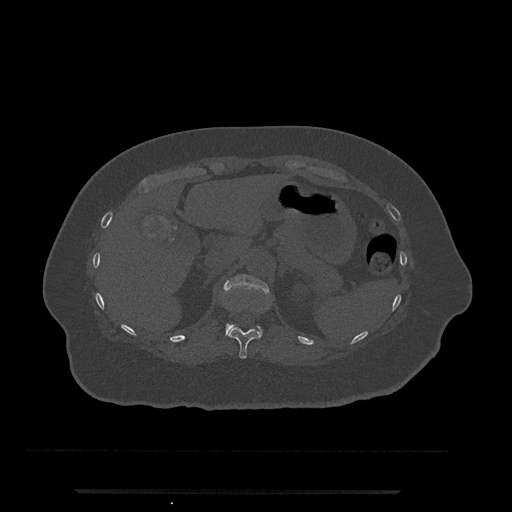
CT including the spine, one axial slice; position 205 of 797 along the scan axis; bone window (W 1800 / L 400 HU); 0.5 mm slice thickness; 512 × 512 image matrix, field of view 440 × 440 mm. Patient: female, 51 years. From the clinical record (not read from this slice): primary cancer: neuro.
Annotated regions visible in this slice (semi-automatic segmentation, software-assisted and operator-edited):
- T11 vertebra: box from (x=227, y=327) to (x=261, y=359) px
- T12 vertebra: (x=224, y=274)–(x=269, y=335)